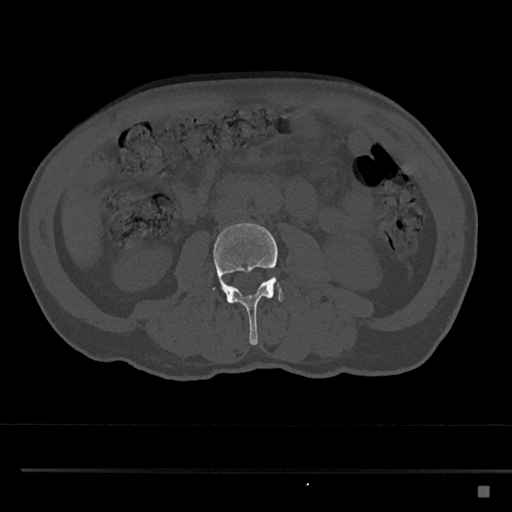
CT including the spine, one axial slice. Slice 690 of 797 in the series (ordered by position). 120 kVp. Bone window (W 1800 / L 400 HU). 0.5 mm slice thickness. 512 × 512 image matrix. Male patient, age 59 years. Case-level facts recorded for this patient, not image findings: primary cancer: prostate.
Structures marked on this image (semi-automatic segmentation, software-assisted and operator-edited):
- L3 vertebra: bounding box (x1, y1, x2, y2) in pixels: (212, 223, 282, 345)
- L4 vertebra: (278, 281, 284, 302)